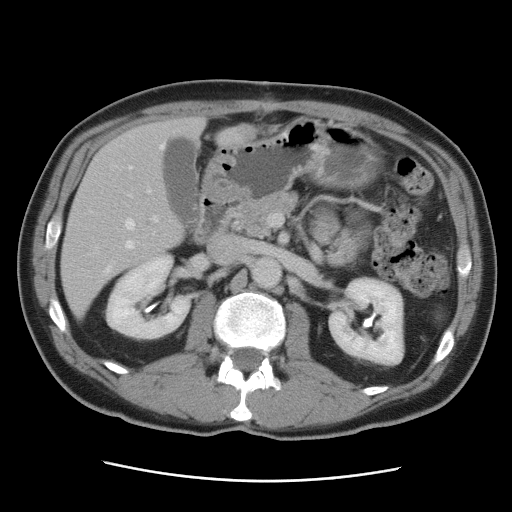
Contrast-enhanced abdominal CT, one axial slice. Slice 44 of 89 in the series (ordered by position). 120 kVp. Intravenous contrast given. Soft-tissue window (W 400 / L 40 HU). 512 × 512 image matrix, field of view 366 × 366 mm. Male patient, age 59 years. Case-level facts recorded for this patient, not image findings: diagnosis: colorectal cancer liver metastases, imaged before liver resection; multiple liver metastases: yes; largest metastasis: 0.6 cm; disease in both lobes: yes.
Outlined on this slice (manually delineated by an expert):
- hepatic veins: bounding box [x1, y1, x2, y2] px = [91, 144, 165, 273]
- liver: [63, 118, 255, 319]
- planned liver remnant (the part of the liver to remain after resection): [72, 118, 203, 245]
- portal vein (with intrahepatic branches): [129, 188, 158, 222]
- liver metastasis: [235, 127, 252, 139]